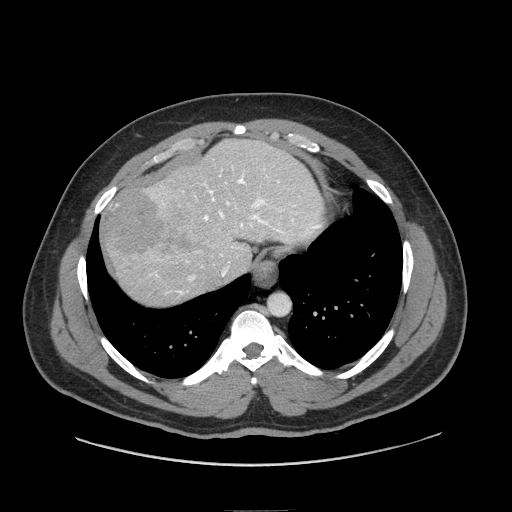
Contrast-enhanced abdominal CT (liver protocol), one axial slice; reconstruction kernel STANDARD; 140 kVp; soft-tissue window (W 400 / L 40 HU); 2.5 mm slice thickness; 512 × 512 image matrix. From the clinical record (not read from this slice): diagnosis: hepatocellular carcinoma (patient treated with transarterial chemoembolisation; whether this scan precedes or follows treatment is not stated here); TNM stage (as recorded): Stage-II; Child-Pugh class: A; tumour differentiation: moderately differentiated.
Outlined on this slice (semi-automatic segmentation, software-assisted and operator-edited):
- liver parenchyma outside the tumour (the mass and vessels are separate outlines, so this box may not span the whole liver): box from (x=104, y=140) to (x=322, y=304) px
- mass: (x=102, y=184)–(x=195, y=261)
- liver vessels: (x=156, y=169)–(x=320, y=295)